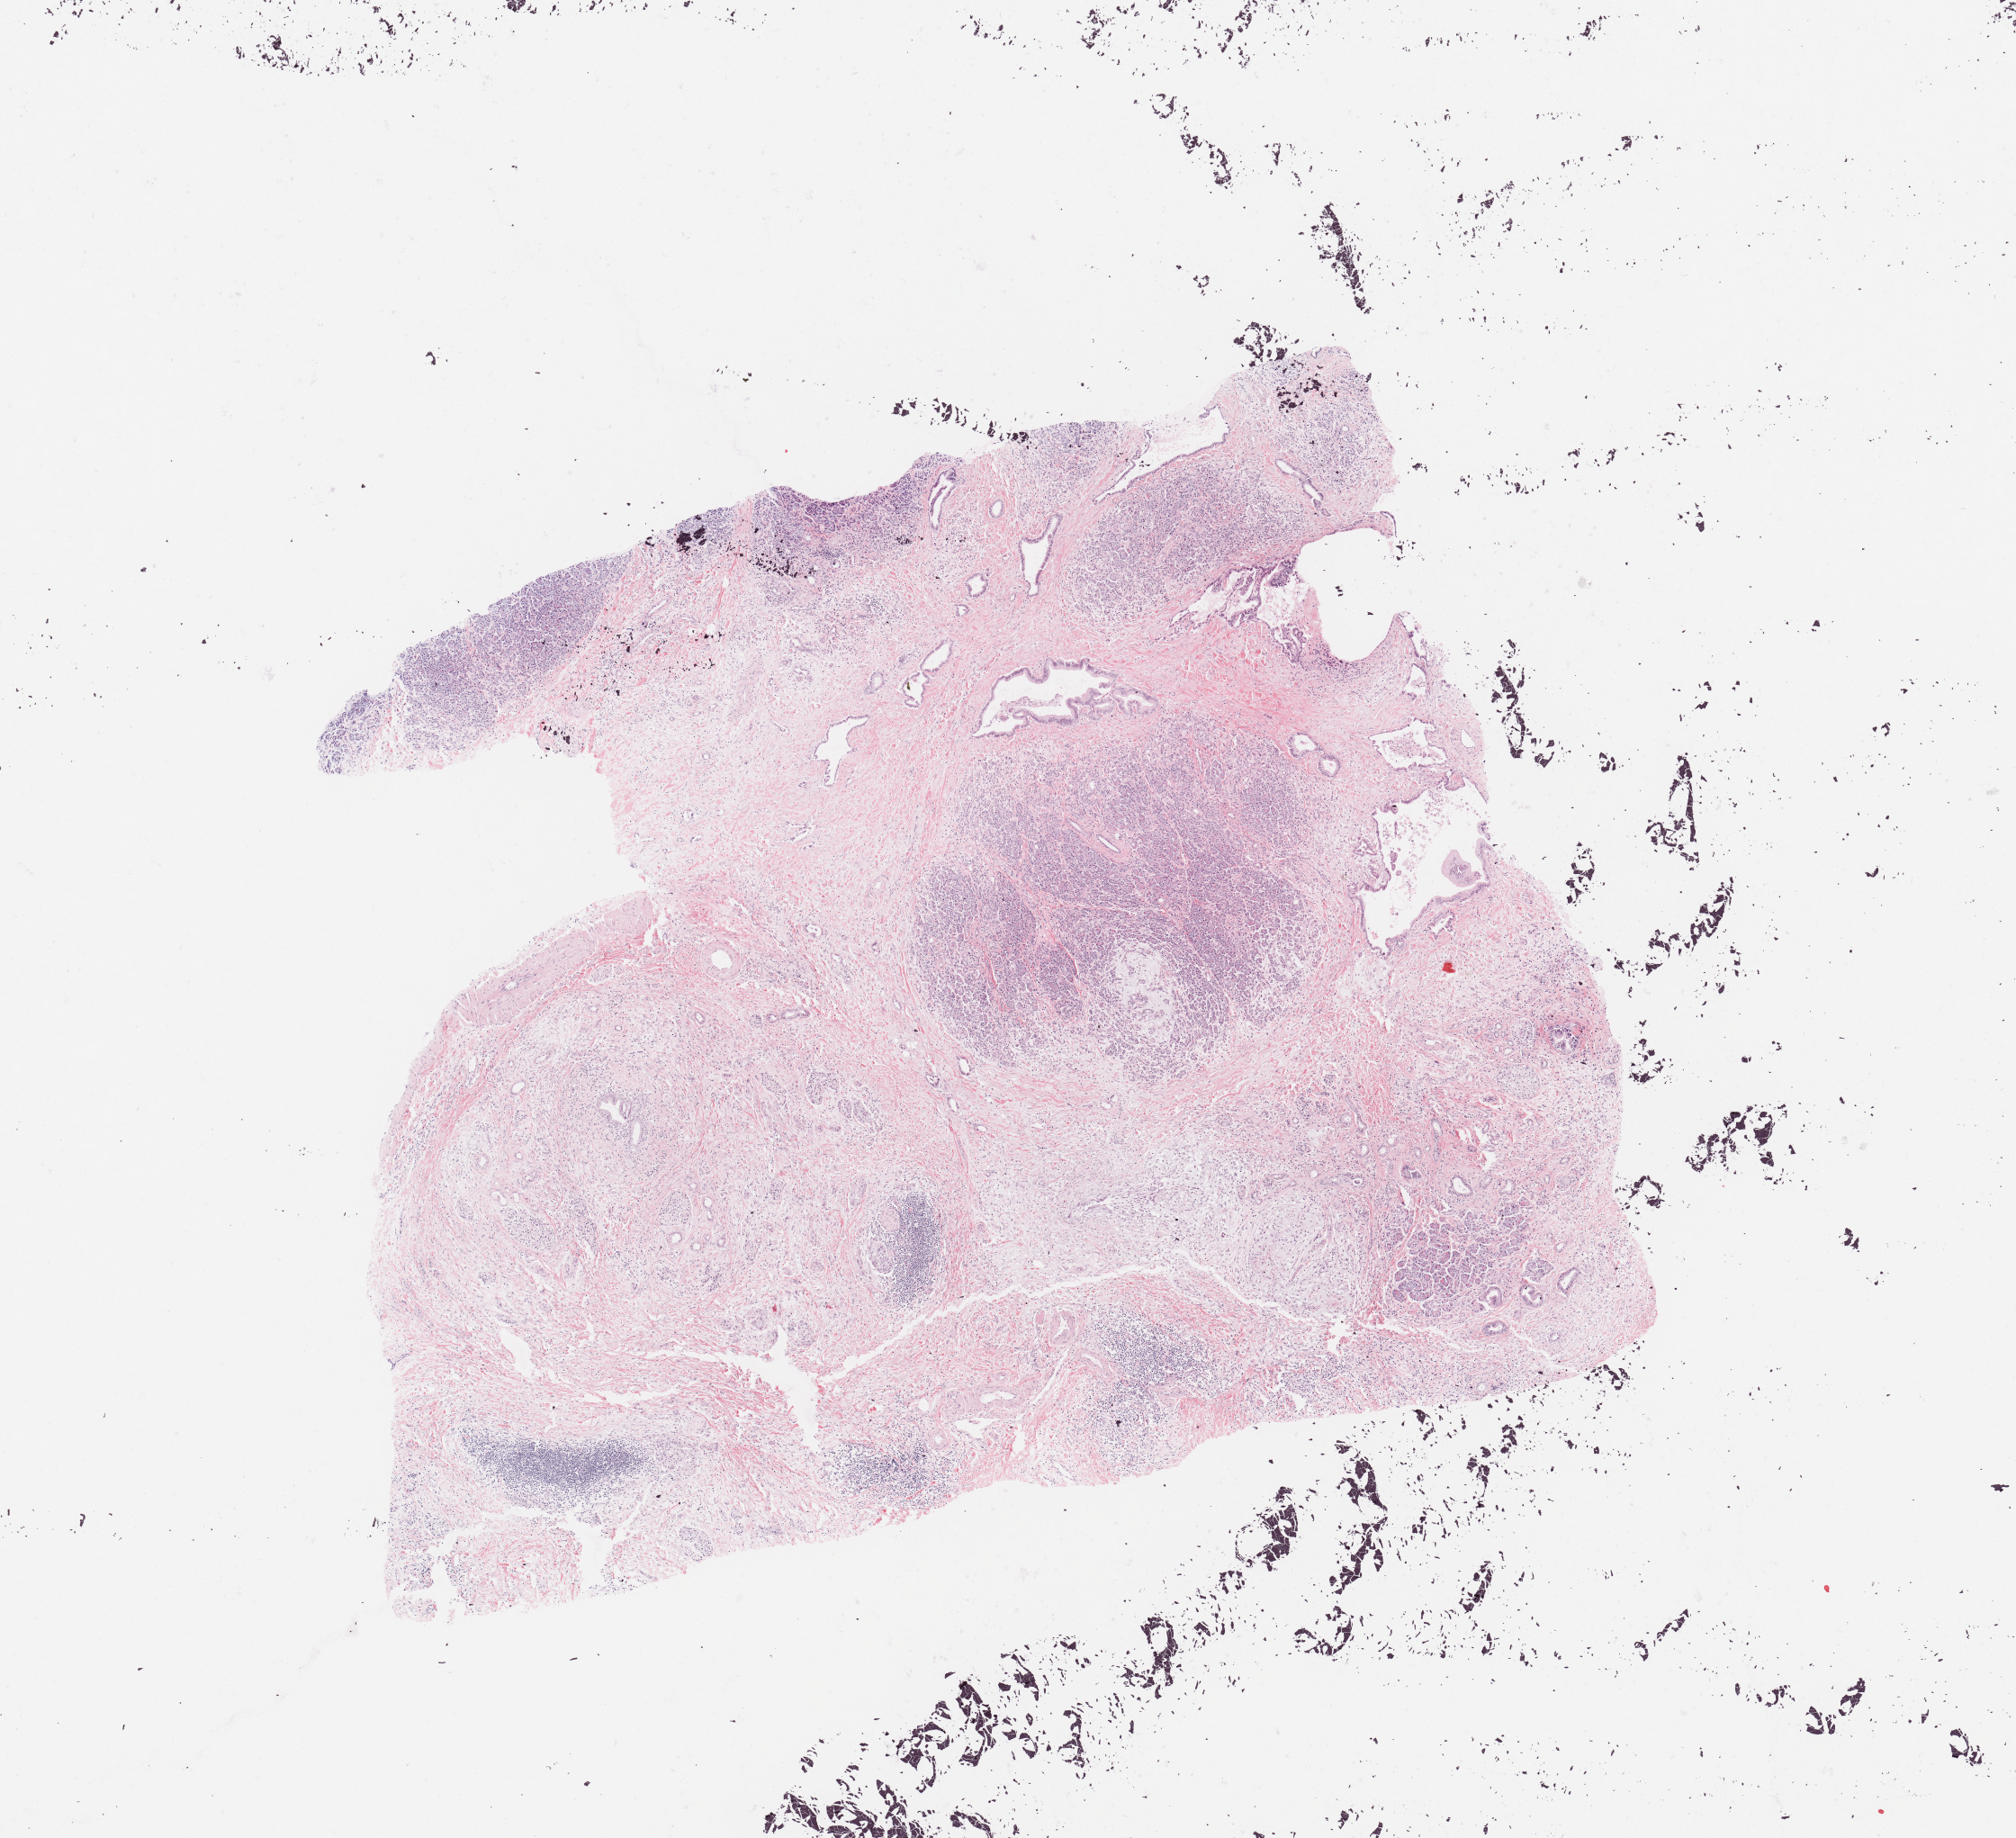
Whole-slide histology image, H&E-stained, low-resolution overview of the scanned area, about 8.9 x 8.1 mm; tumour tissue sample, pancreas. Female, 67 y/o.
Primary tumour site (as recorded): head. Patient diagnosis (cohort enrolment): ductal adenocarcinoma (pancreas).